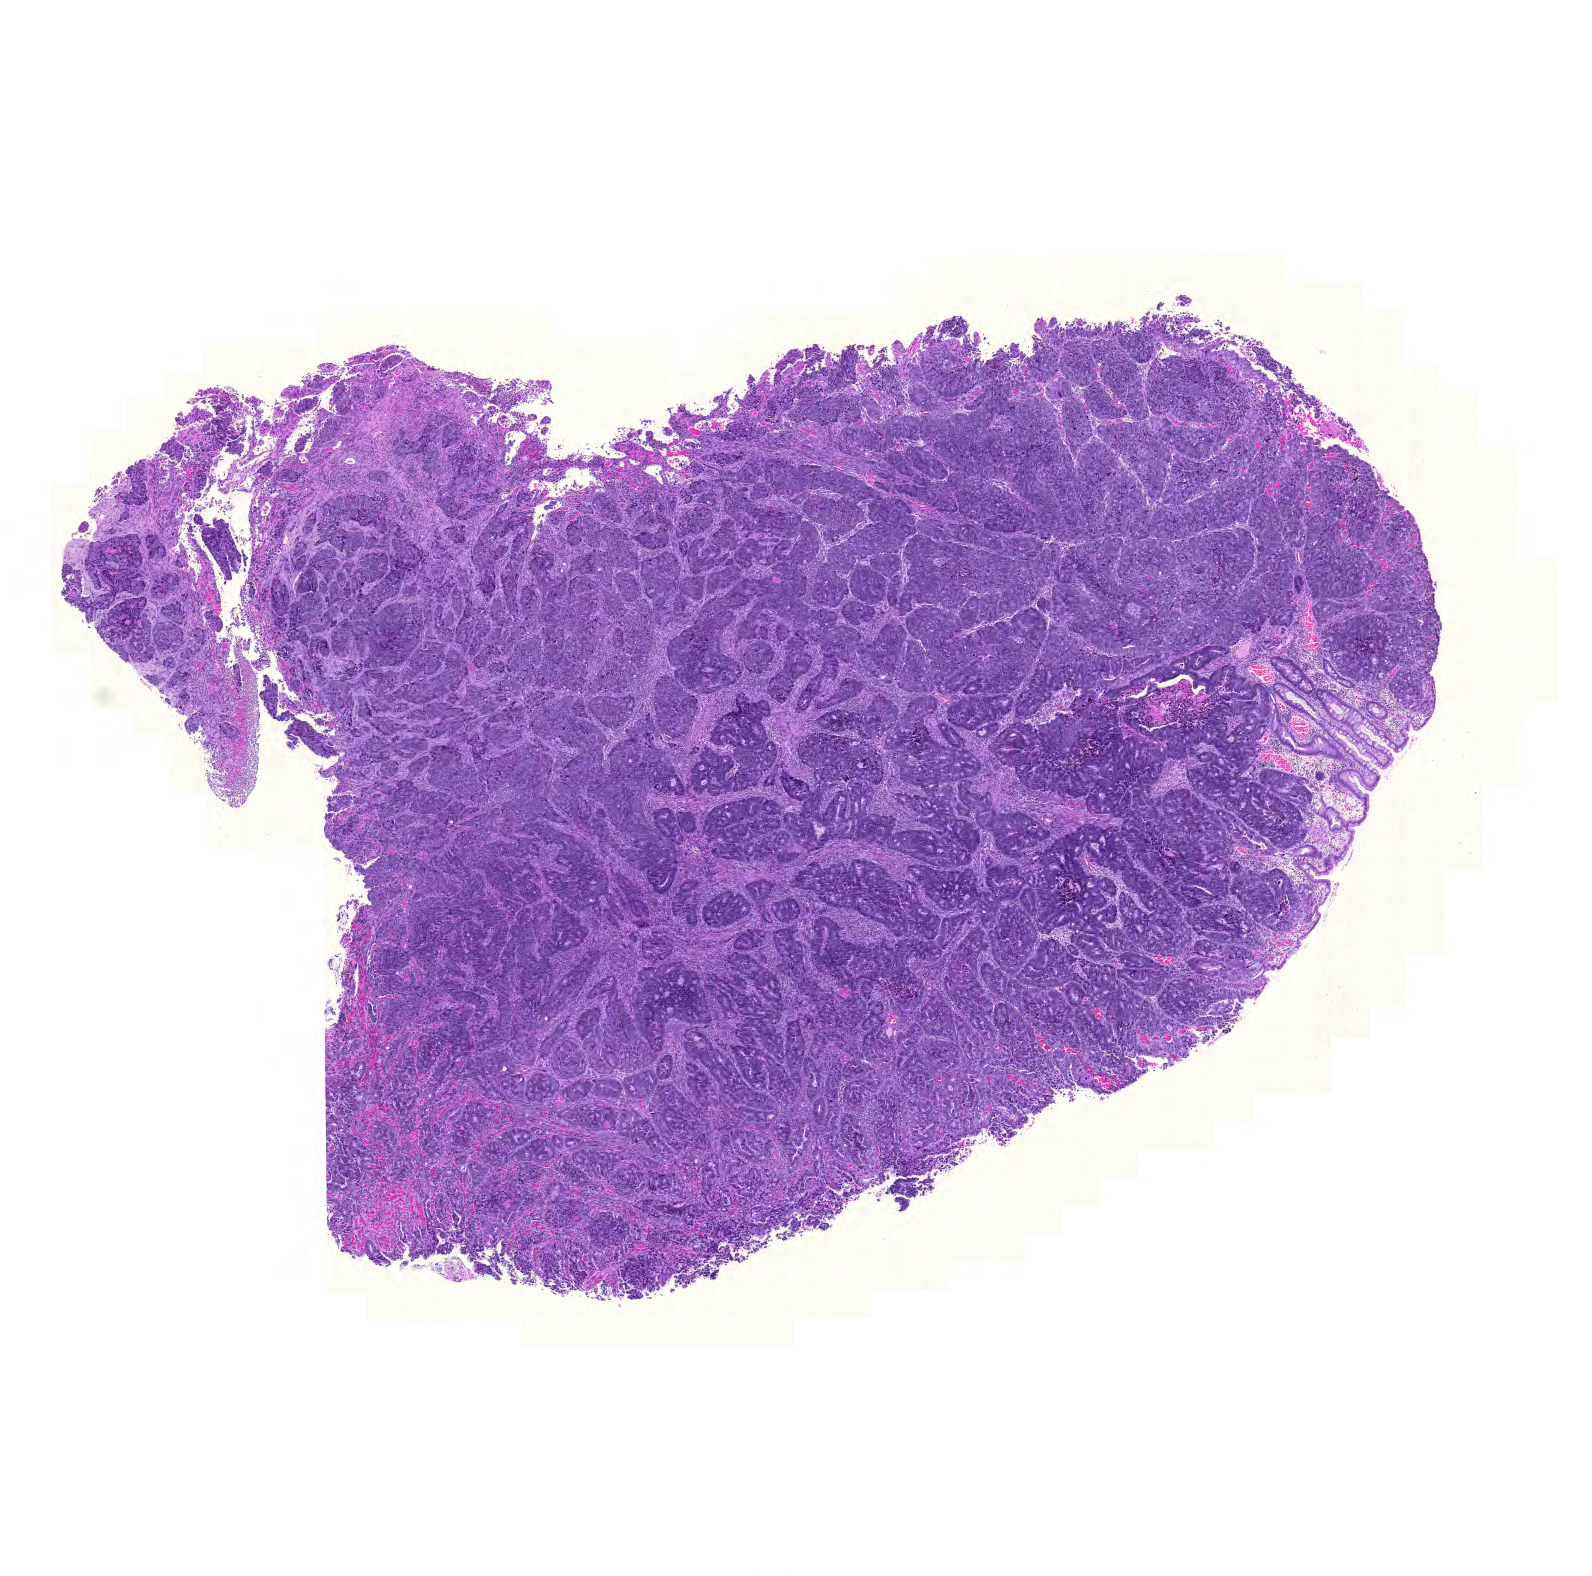
Whole-slide histology image, Hematoxylin and eosin (H&E) stained, a low-resolution overview of the entire scanned area, about 11.8 x 11.7 mm. Formalin-fixed paraffin-embedded (FFPE) diagnostic section. Colon, primary tumour sample. Patient: male, age at initial diagnosis 69 years.
Pathologic diagnosis: Adenocarcinoma, NOS (sigmoid colon). AJCC pathologic stage: IIIC (6th edition).